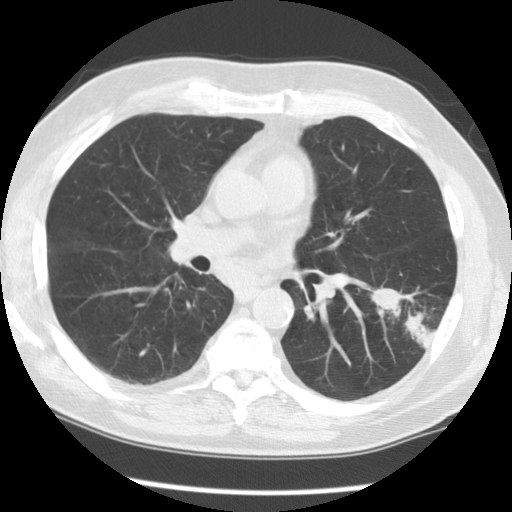
Low-dose screening chest CT, one axial slice; position 74 of 130 along the scan axis; 120 kVp; lung window (W 1500 / L -600 HU); 2.5 mm slice thickness; 512 × 512 image matrix, field of view 340 × 340 mm.
Annotated regions visible in this slice (manually delineated by an expert):
- lesion 1 (tumor, lower lobe of left lung): bounding box (x1, y1, x2, y2) in pixels: (371, 288, 435, 348)